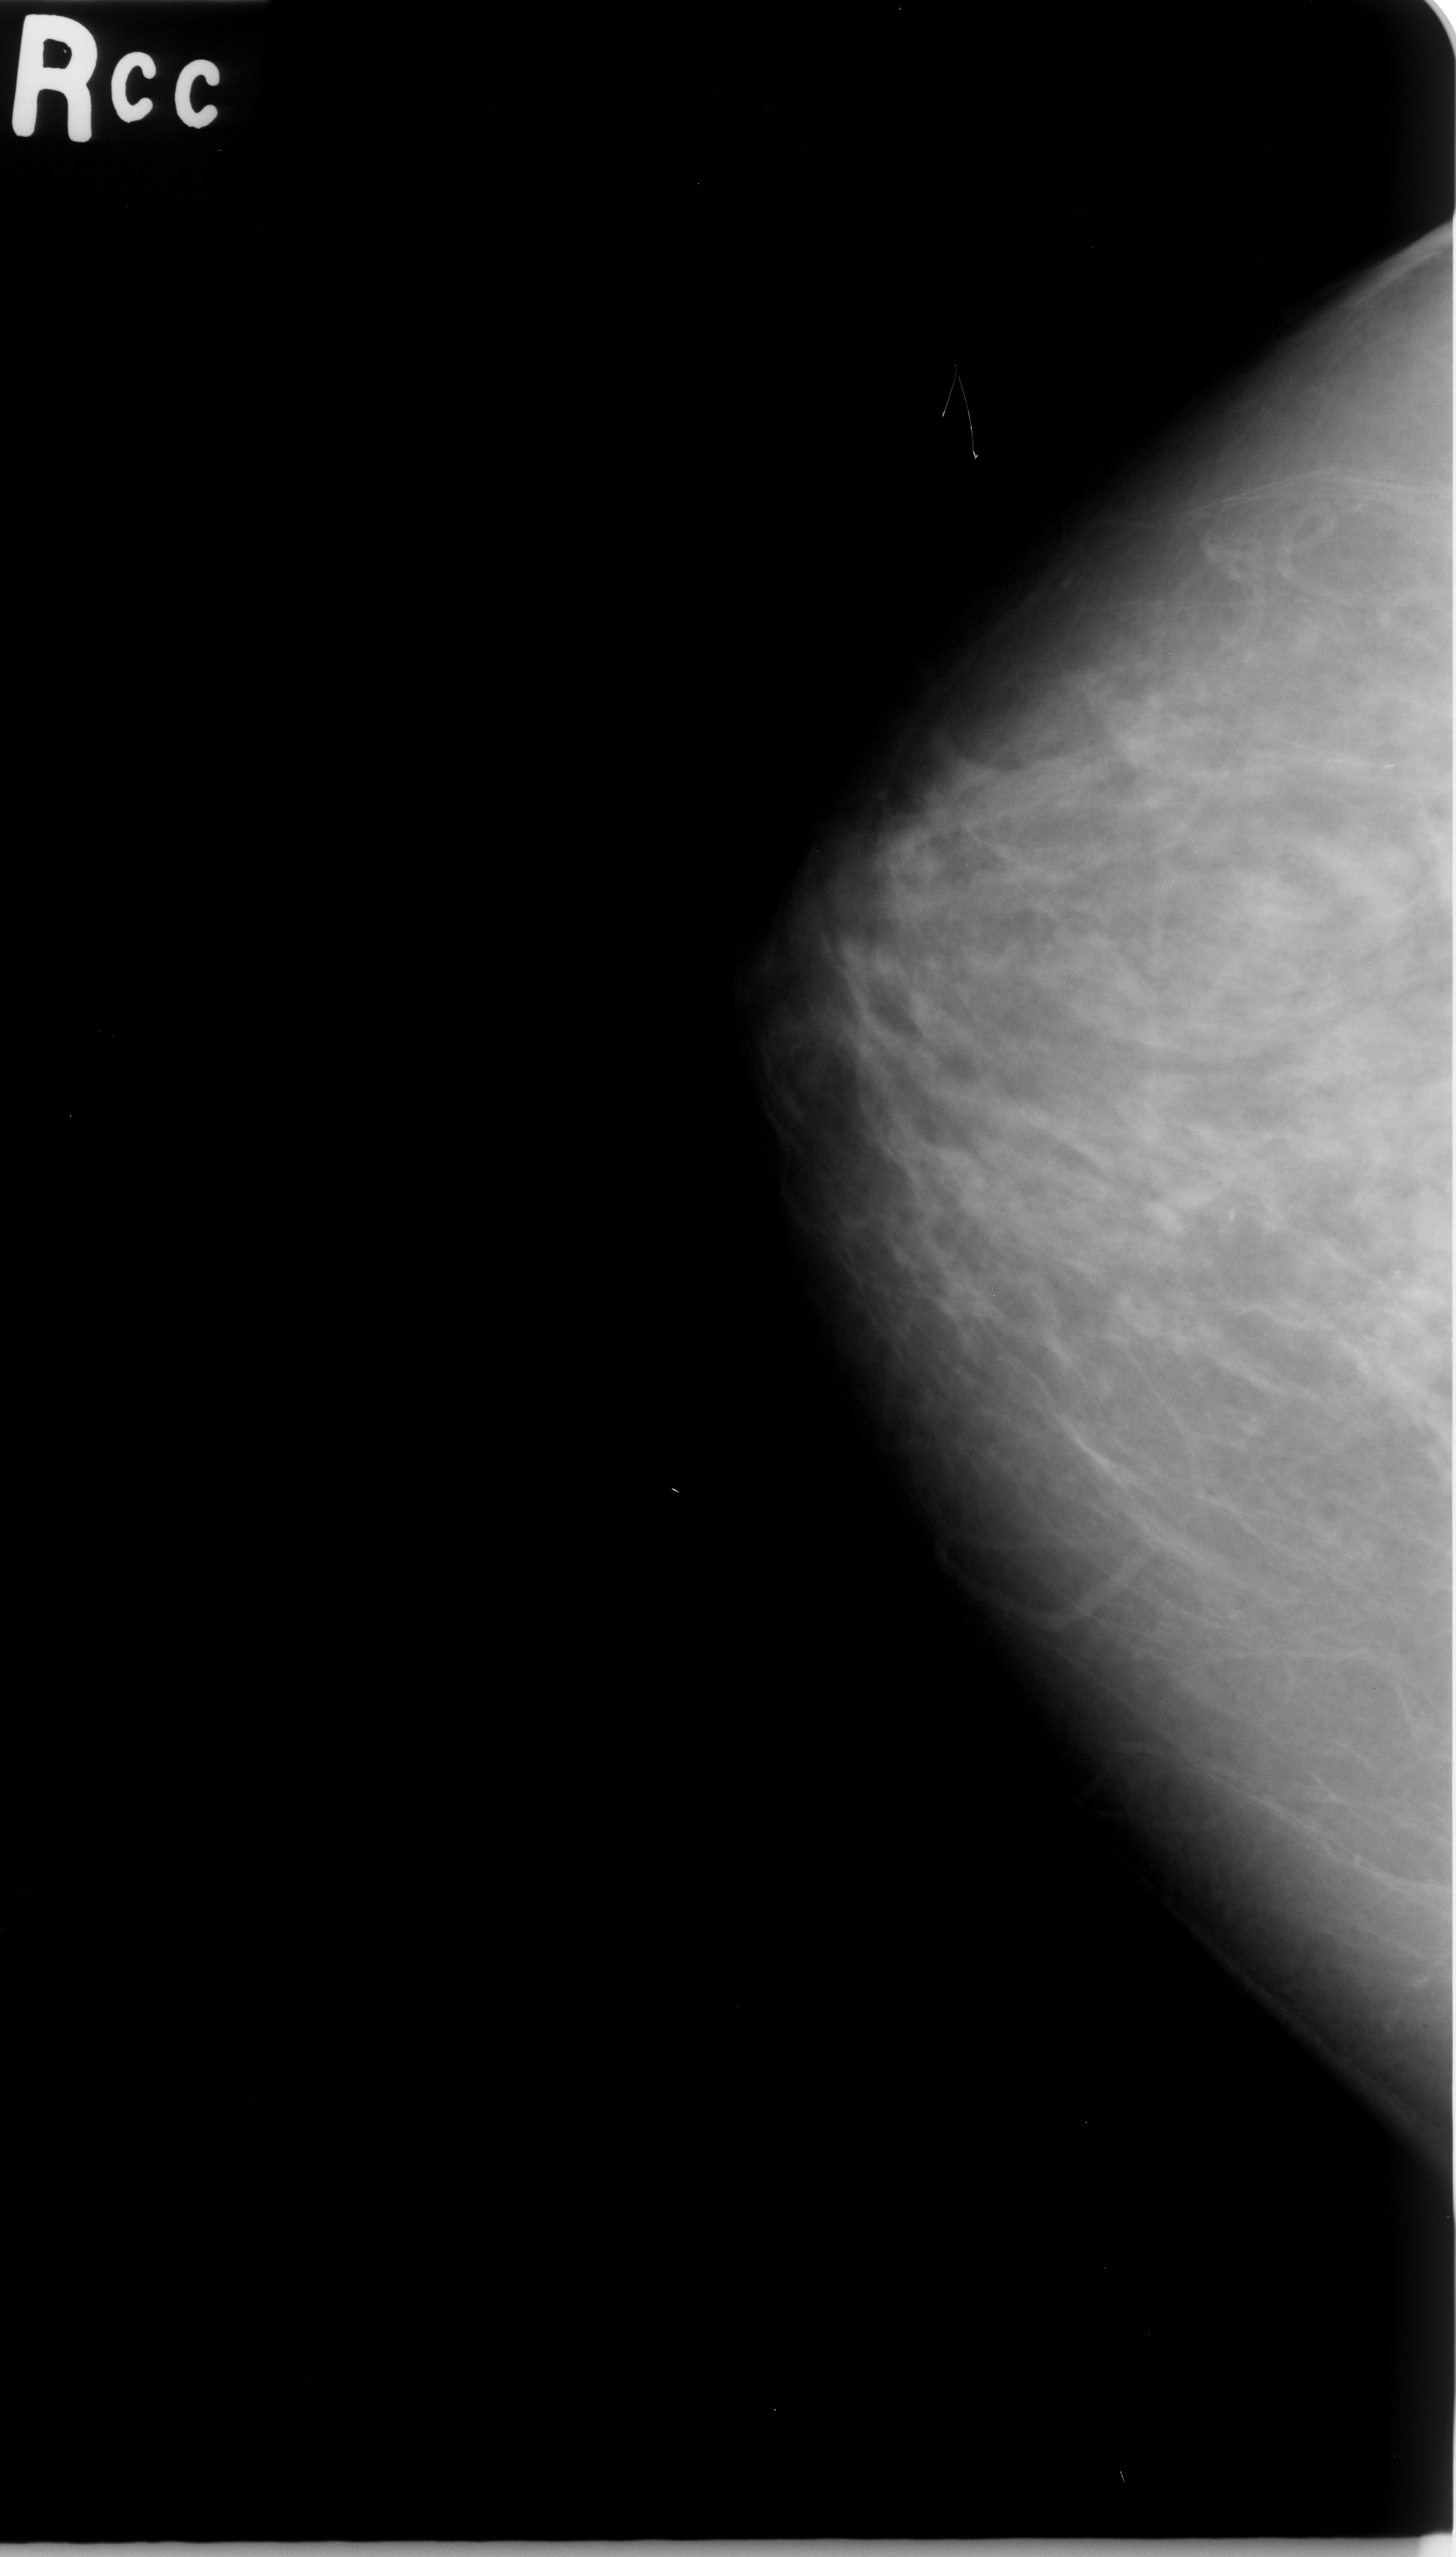
Scanned film-screen mammogram. Right breast. Craniocaudal (CC) view. Breast composition: scattered fibroglandular densities (BI-RADS density category 2 of 4). 1456 × 2557 image matrix.
Marked abnormalities (boxes around the expert regions of interest):
- calcifications, morphology pleomorphic, distribution clustered; BI-RADS assessment category 5; subtlety rating 4 on a 1 (subtle) to 5 (obvious) scale; pathology result (as recorded, not read from the image): malignant: bounding box (x1, y1, x2, y2) in pixels: (1247, 1198, 1453, 1541)